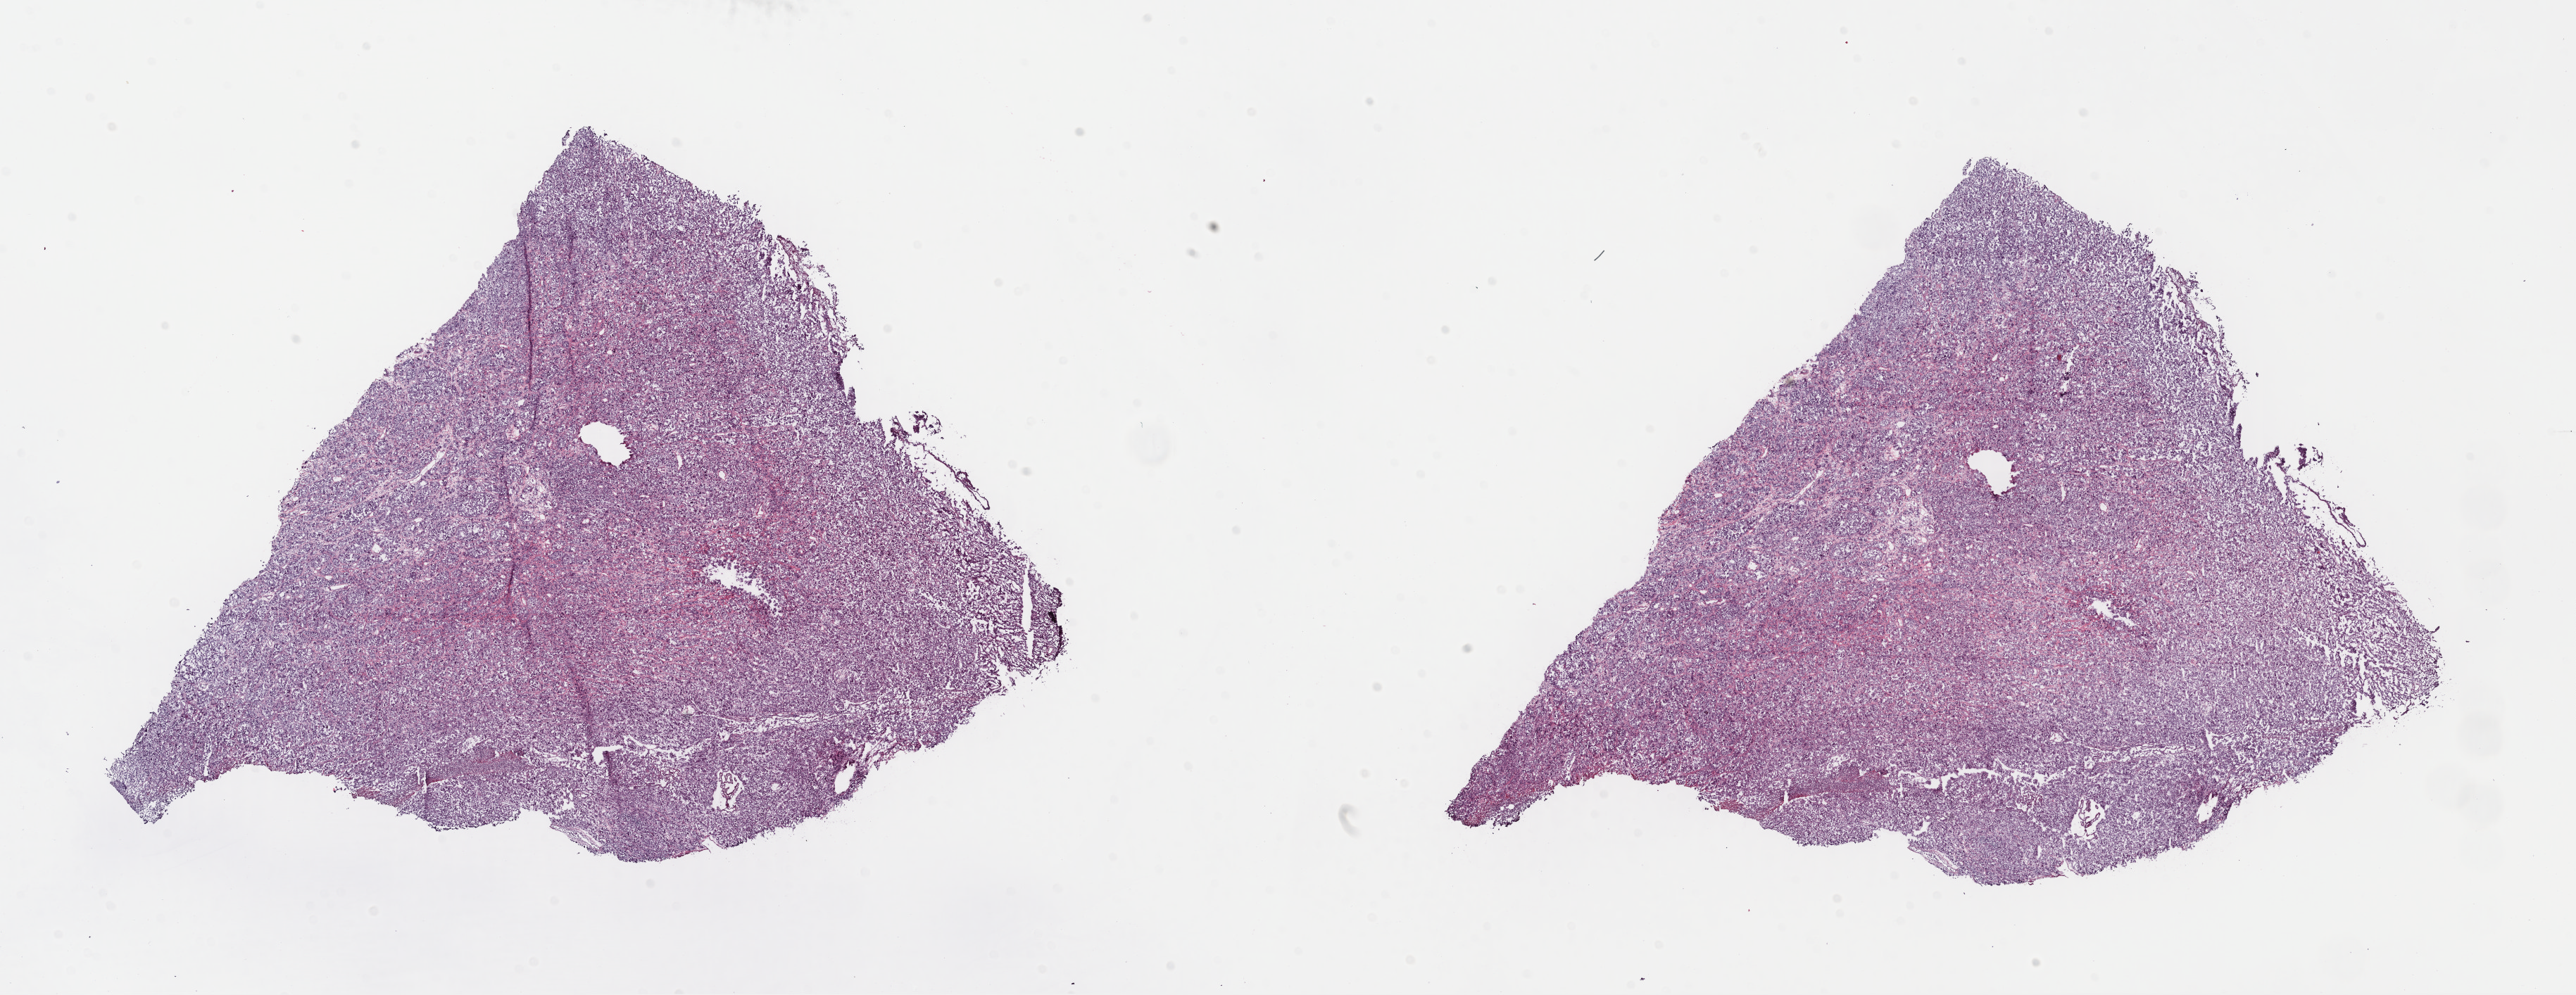
Whole-slide histology image, H&E-stained, a low-resolution overview of the entire scanned area, about 28.8 x 11.1 mm (from a 40x scan); frozen section; metastatic tumour sample, sampled site not recorded. Male patient; age at initial diagnosis 49 years. Pathologist review of this section (percent, as recorded): tumour cells 100%, tumour nuclei 80%, normal cells 0%, stromal cells 0%, necrosis 0%. Infiltration values recorded for this section: lymphocyte infiltration 2%, monocyte infiltration 0%, neutrophil infiltration 0%.
• this section: metastatic tumour tissue
• patient diagnosis: Malignant melanoma, NOS